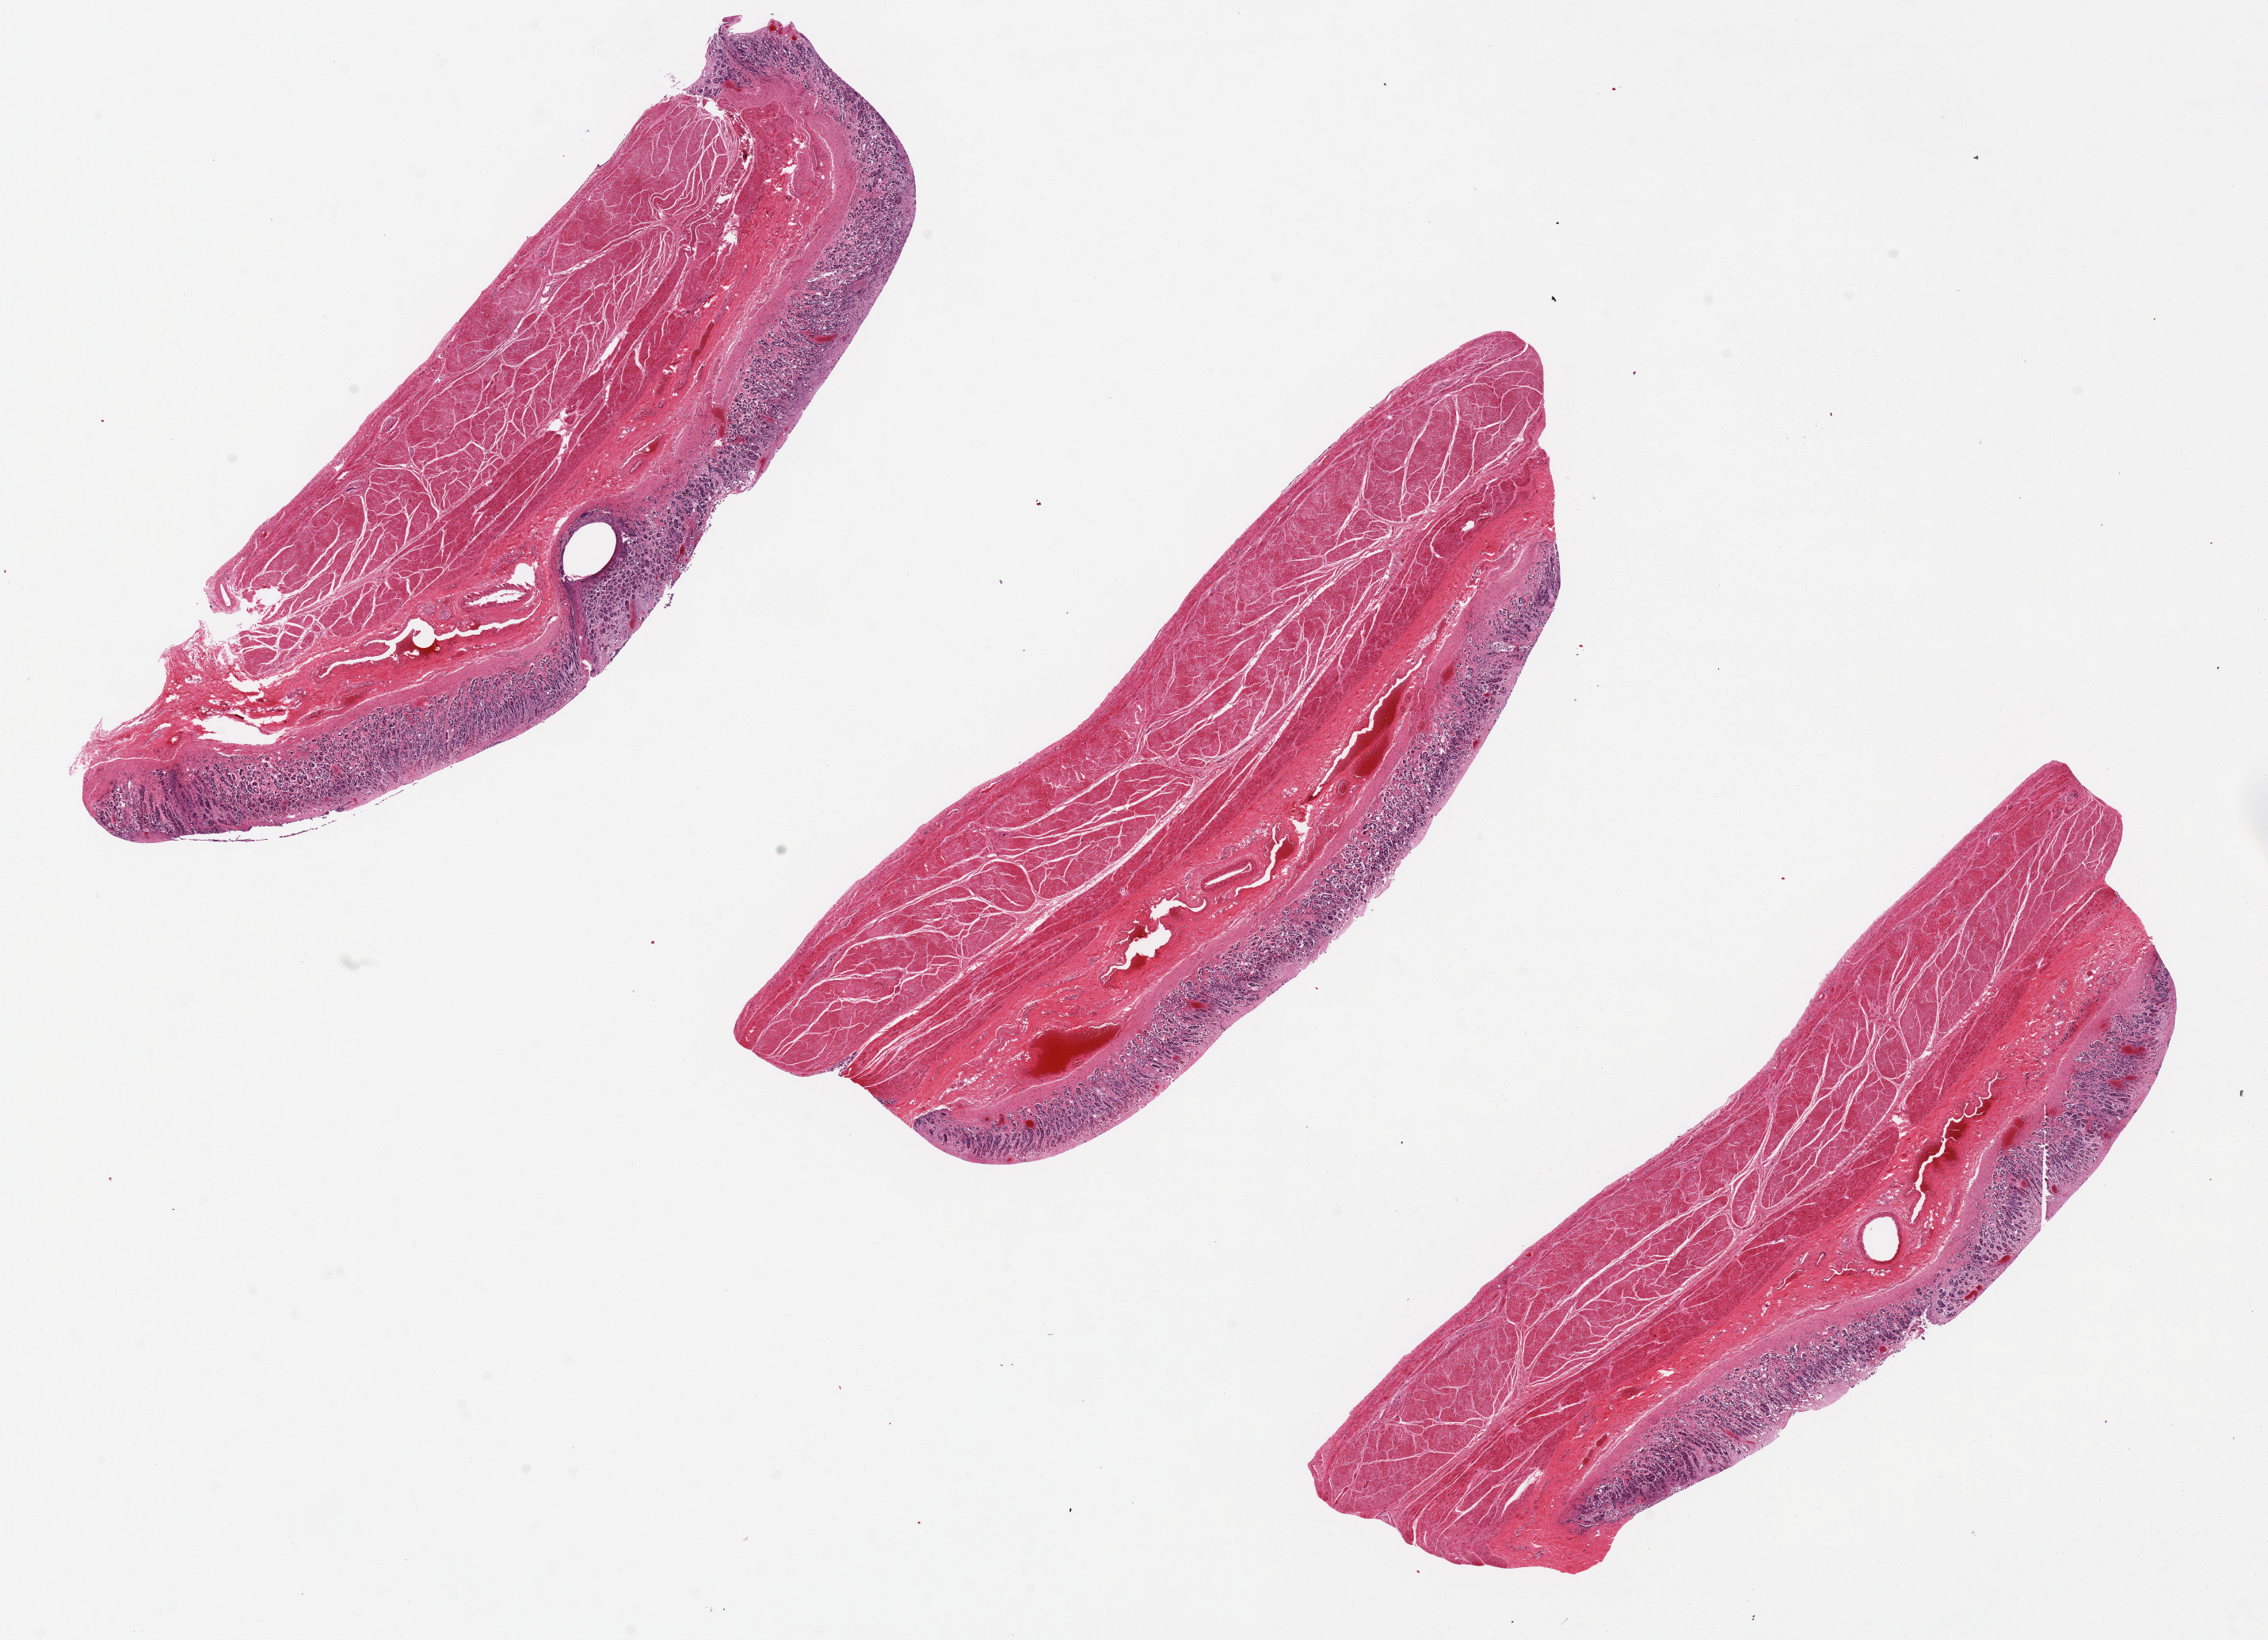
Haematoxylin and eosin whole-slide image — low-resolution overview of the scanned area, about 22.6 x 16.4 mm (acquisition: 20x scan), PAXgene-fixed, paraffin-embedded tissue, sampled site (target tissue): stomach, tissue donor sample.
Reviewer comment on this tissue sample: Mucosa is 8-10% total thickness. 3 pieces 10x3.3mm.